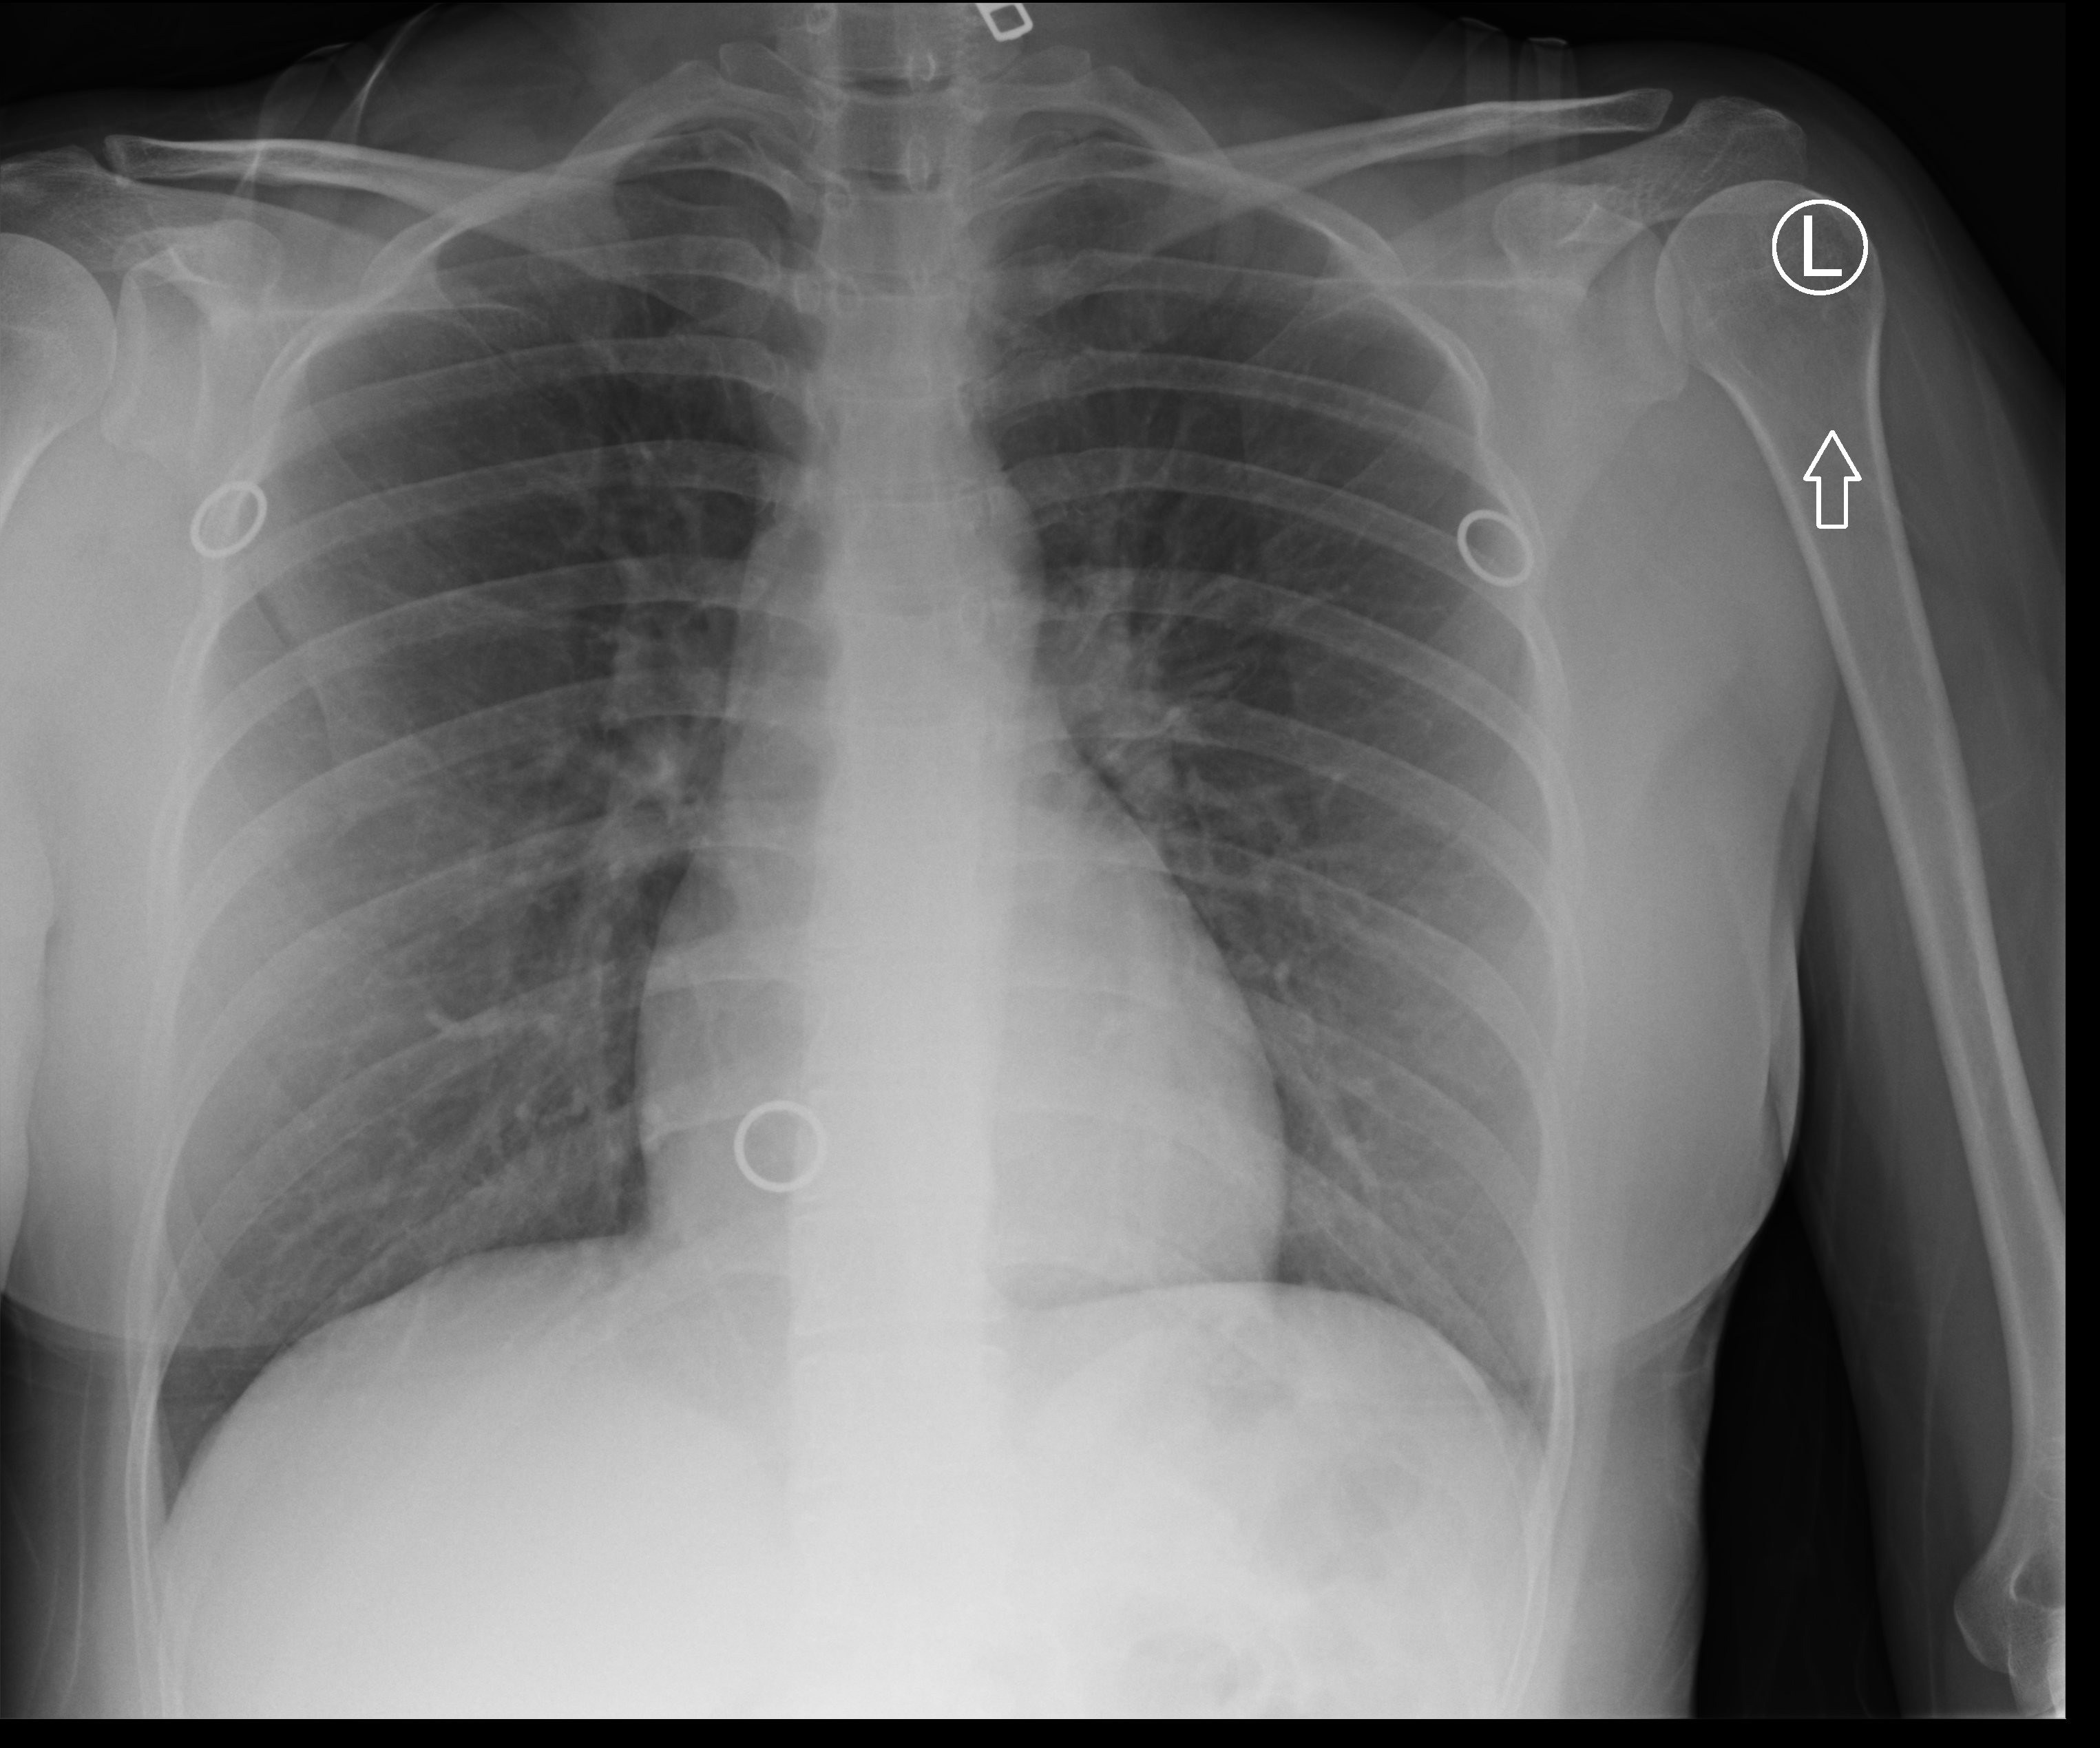
Bedside chest radiograph (computed radiography); anteroposterior (AP) projection. Patient hospitalised with COVID-19; female, aged 18–59 years.
From the hospital-stay record, not from the radiograph (when in the stay this image was taken is not recorded): admitted to intensive care during this hospital stay: no; mechanically ventilated during this hospital stay: no.